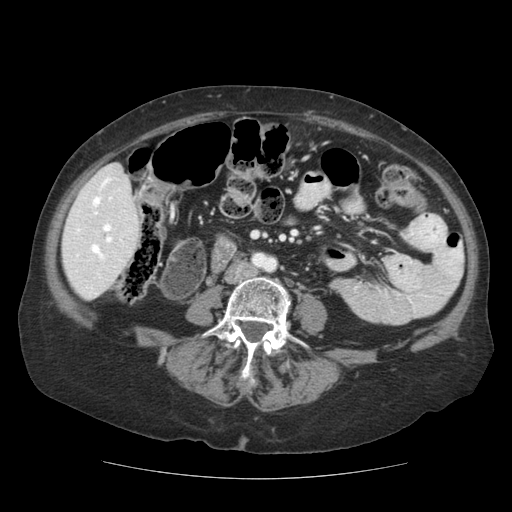
Contrast-enhanced abdominal CT (liver protocol), one axial slice. Slice 34 of 111 in the series (ordered by position). Reconstruction kernel STANDARD. Soft-tissue window (W 400 / L 40 HU). 2.5 mm slice thickness. 512 × 512 image matrix. Case-level facts recorded for this patient, not image findings: diagnosis: hepatocellular carcinoma (patient treated with transarterial chemoembolisation; whether this scan precedes or follows treatment is not stated here); TNM stage (as recorded): Stage-I; Child-Pugh class: A; tumour differentiation: moderately-poorly differentiated; tumour size: 7.3 cm.
Outlined on this slice (semi-automatic segmentation, software-assisted and operator-edited):
- liver parenchyma outside the tumour (the mass and vessels are separate outlines, so this box may not span the whole liver): bounding box (x1, y1, x2, y2) in pixels: (62, 163, 140, 300)
- liver vessels: (75, 177, 131, 261)